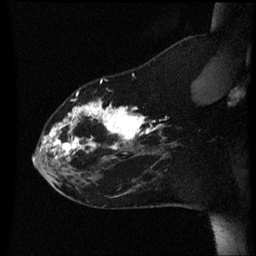
Breast MRI (dynamic contrast-enhanced), one sagittal slice. Position 17 of 60 along the scan axis. Dynamic contrast-enhanced series, image 2 of 3 at this slice position (ordered by acquisition). 1.5 T. TE 4.2 ms, TR 8.4 ms. 2.2 mm slice thickness. 256 × 256 image matrix, field of view 200 × 200 mm. Female patient, age 35 years. From the clinical record (not read from this slice): setting: breast cancer imaged before/during neoadjuvant chemotherapy; receptor status: HER2-positive.
Annotated regions visible in this slice (semi-automatic segmentation, software-assisted and operator-edited):
- analysis volume of interest (the breast-tissue region the enhancement analysis was run in; not a lesion): bounding box (x1, y1, x2, y2) in pixels: (34, 72, 178, 173)
- tumour enhancement mask (voxels above the 70 % enhancement threshold inside the analysis volume of interest): (44, 80, 165, 159)